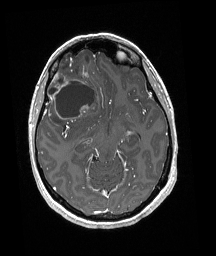
Brain MRI from a brain-tumour surgery series, one axial slice. T1-weighted post-contrast. 1 mm slice thickness. 216 × 256 image matrix, field of view 211 × 250 mm. From the clinical record (not read from this slice): histopathology: Oligodendroglioma; WHO grade: 3.
Structures marked on this image (expert manual segmentation):
- tumour: bounding box [x1, y1, x2, y2] px = [45, 53, 98, 125]